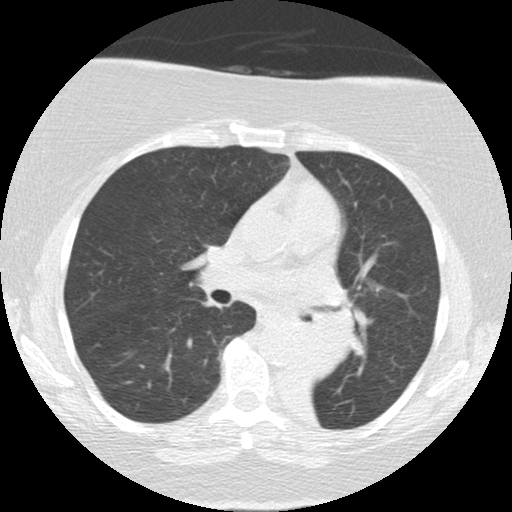
Low-dose screening chest CT, one axial slice. Slice 77 of 136 in the series (ordered by position). Reconstruction kernel STANDARD. 120 kVp. Lung window (W 1500 / L -600 HU). 2.5 mm slice thickness. 512 × 512 image matrix, field of view 309 × 309 mm.
Annotated regions visible in this slice (expert manual segmentation):
- lesion 2 (tumor, mediastinum): bounding box <300,280,354,381> (left, top, right, bottom; pixels)